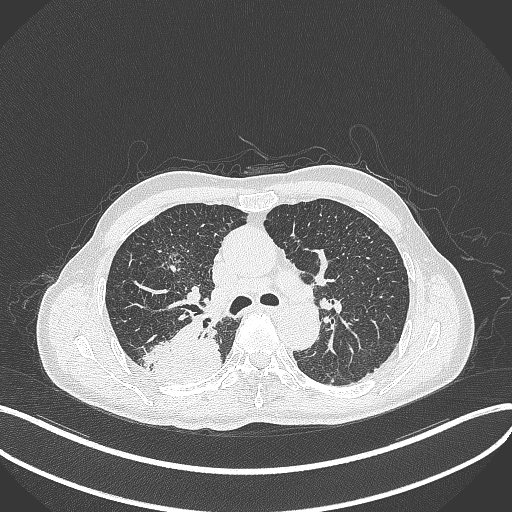
Chest CT, one axial slice. Slice 297 of 428 in the series (ordered by position). Reconstruction kernel B70f. 120 kVp. Lung window (W 1500 / L -600 HU). 1 mm slice thickness. 512 × 512 image matrix, field of view 400 × 400 mm. Male patient, age 79 years. Case-level facts recorded for this patient, not image findings: clinical TNM (as recorded): T3 N0 M0.
Structures marked on this image (bounding box drawn by a radiologist):
- lung tumour (recorded histology: adenocarcinoma): bounding box <144,318,223,378> (left, top, right, bottom; pixels)